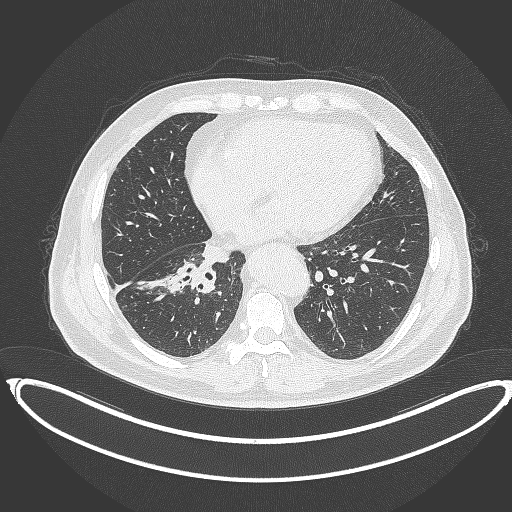
Chest CT, one axial slice; position 155 of 387 along the scan axis; 120 kVp; lung window (W 1500 / L -600 HU); 1 mm slice thickness; 512 × 512 image matrix, field of view 448 × 448 mm. Patient: male, 61 years. Case-level facts recorded for this patient, not image findings: clinical TNM (as recorded): T1b N1 M0.
Outlined on this slice (rectangle marked by the reading radiologist):
- lung tumour (recorded histology: squamous cell carcinoma): bounding box <169,259,219,296> (left, top, right, bottom; pixels)